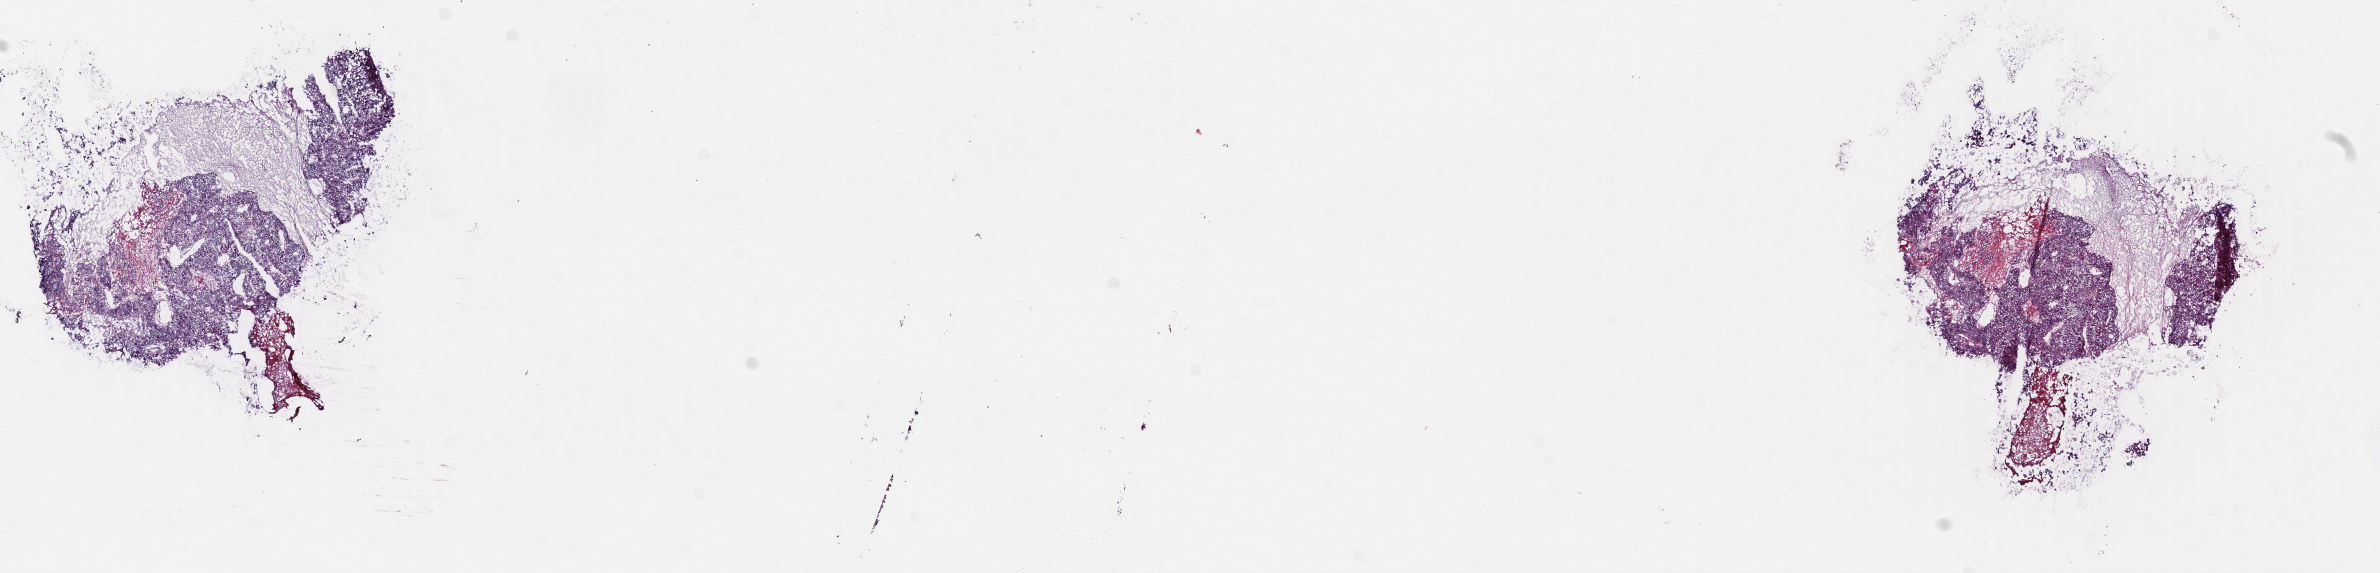
Digitized H&E-stained tissue section (whole slide), shown as a low-resolution overview of the whole scanned area (about 18.7 x 4.5 mm, acquisition: 40x scan); frozen section from the top of the tissue portion; liver, primary tumour sample. Female, age 75 years at initial diagnosis. Histologic grade: G2 (moderately differentiated). Composition of this section per pathologist review: tumour cells 80%, tumour nuclei 80%, normal cells 0%, stromal cells 18%, necrosis 2%. Infiltration values recorded for this section: lymphocyte infiltration 3%, monocyte infiltration 1%, neutrophil infiltration 2%.
AJCC pathologic stage: II (7th edition). Diagnosis: Hepatocellular carcinoma, NOS.